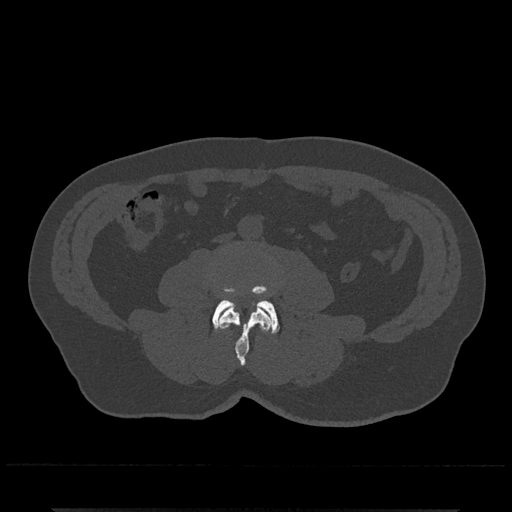
CT including the spine, one axial slice; slice 190 of 797 in the series (ordered by position); 120 kVp; bone window (W 1800 / L 400 HU); 0.5 mm slice thickness; 512 × 512 image matrix, field of view 393 × 393 mm. Patient: male, 67 years. Case-level facts recorded for this patient, not image findings: primary cancer: prostate.
Structures marked on this image (semi-automatic segmentation, software-assisted and operator-edited):
- L3 vertebra: bounding box [x1, y1, x2, y2] px = [218, 306, 272, 365]
- L4 vertebra: [212, 286, 280, 333]